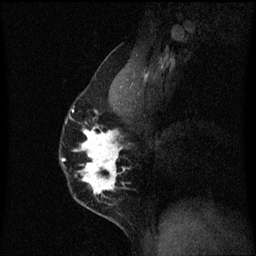
Breast MRI (dynamic contrast-enhanced), one sagittal slice; slice 39 of 60 in the series (ordered by position); dynamic contrast-enhanced series, image 2 of 3 at this slice position (ordered by acquisition); 1.5 T; TE 4.2 ms, TR 8.4 ms; 2 mm slice thickness; 256 × 256 image matrix, field of view 200 × 200 mm. Patient: female, 40 years.
Outlined on this slice (semi-automatic segmentation, software-assisted and operator-edited):
- analysis volume of interest (the breast-tissue region the enhancement analysis was run in; not a lesion): bounding box (x1, y1, x2, y2) in pixels: (61, 88, 126, 211)
- tumour enhancement mask (voxels above the 70 % enhancement threshold inside the analysis volume of interest): (61, 112, 126, 195)